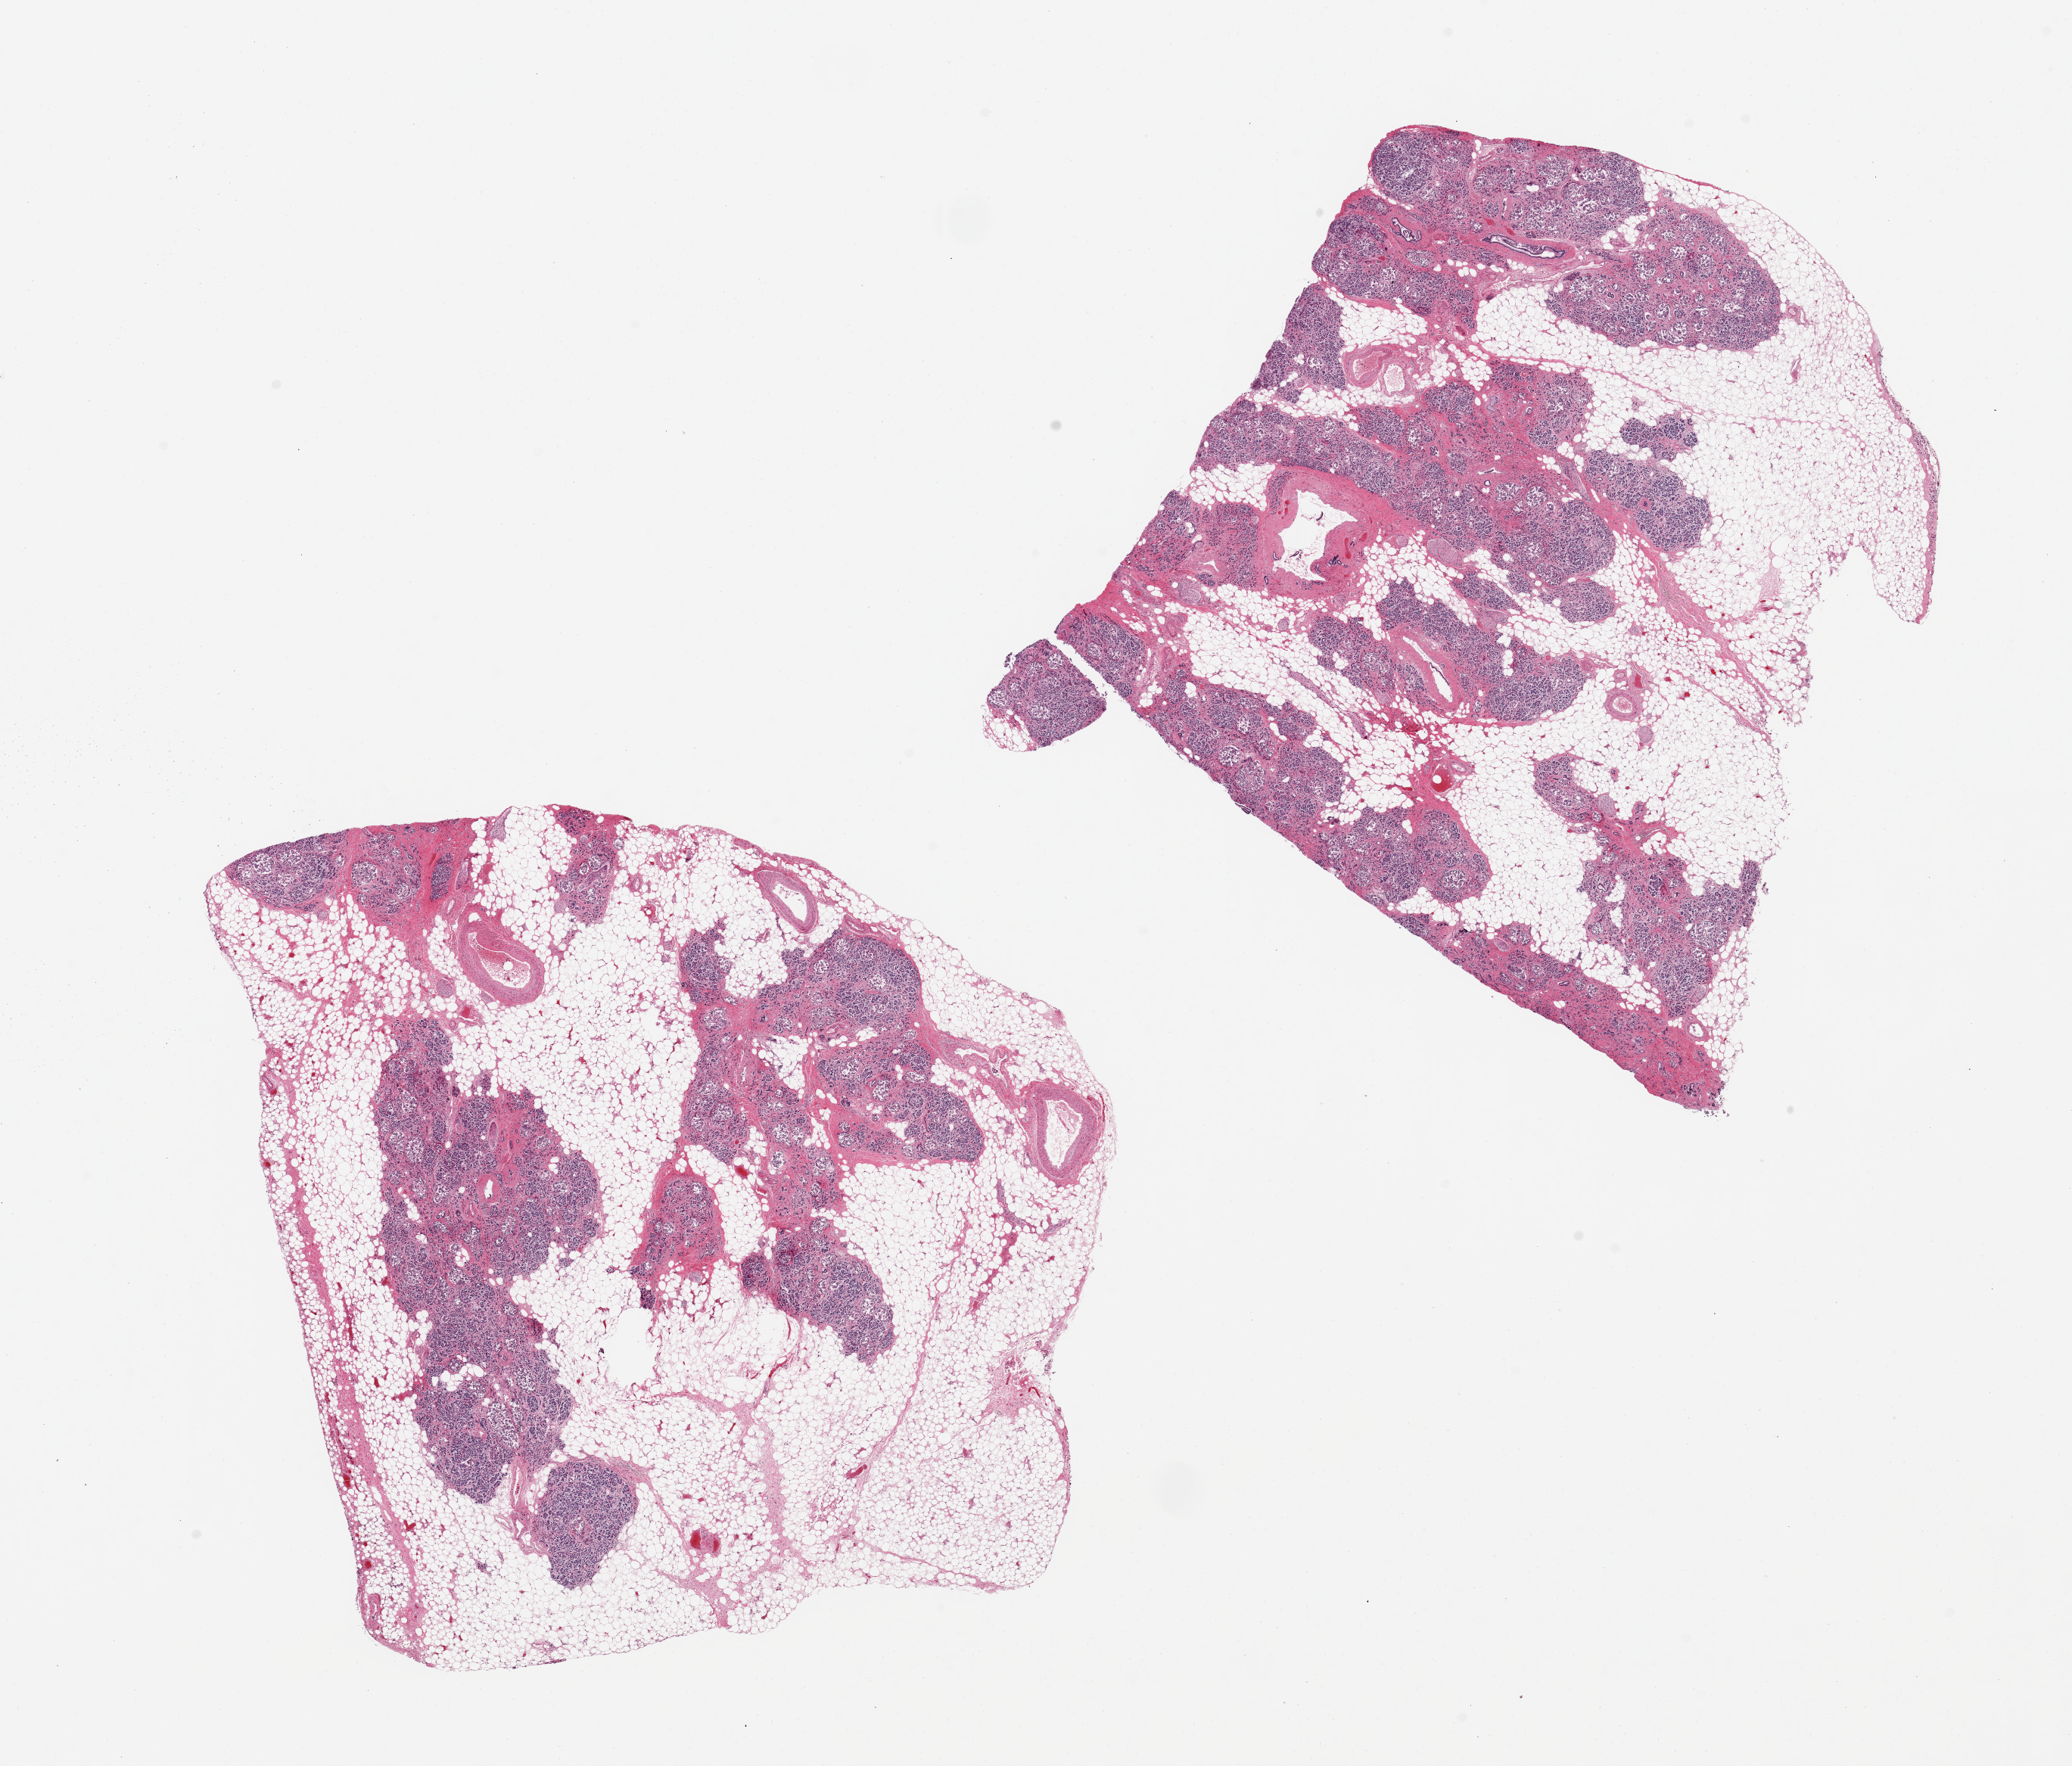
H&E whole-slide image — a low-resolution overview of the entire scanned area, about 21.7 x 18.5 mm; PAXgene-fixed paraffin-embedded (PFPE) section; section of pancreas (target tissue); donor tissue sample.
Pathologist's review note for this sample: 2 pieces 9x9 & 9x8mm; ~50% parenchyma, badly autolyzed, extensive interstitial fat.